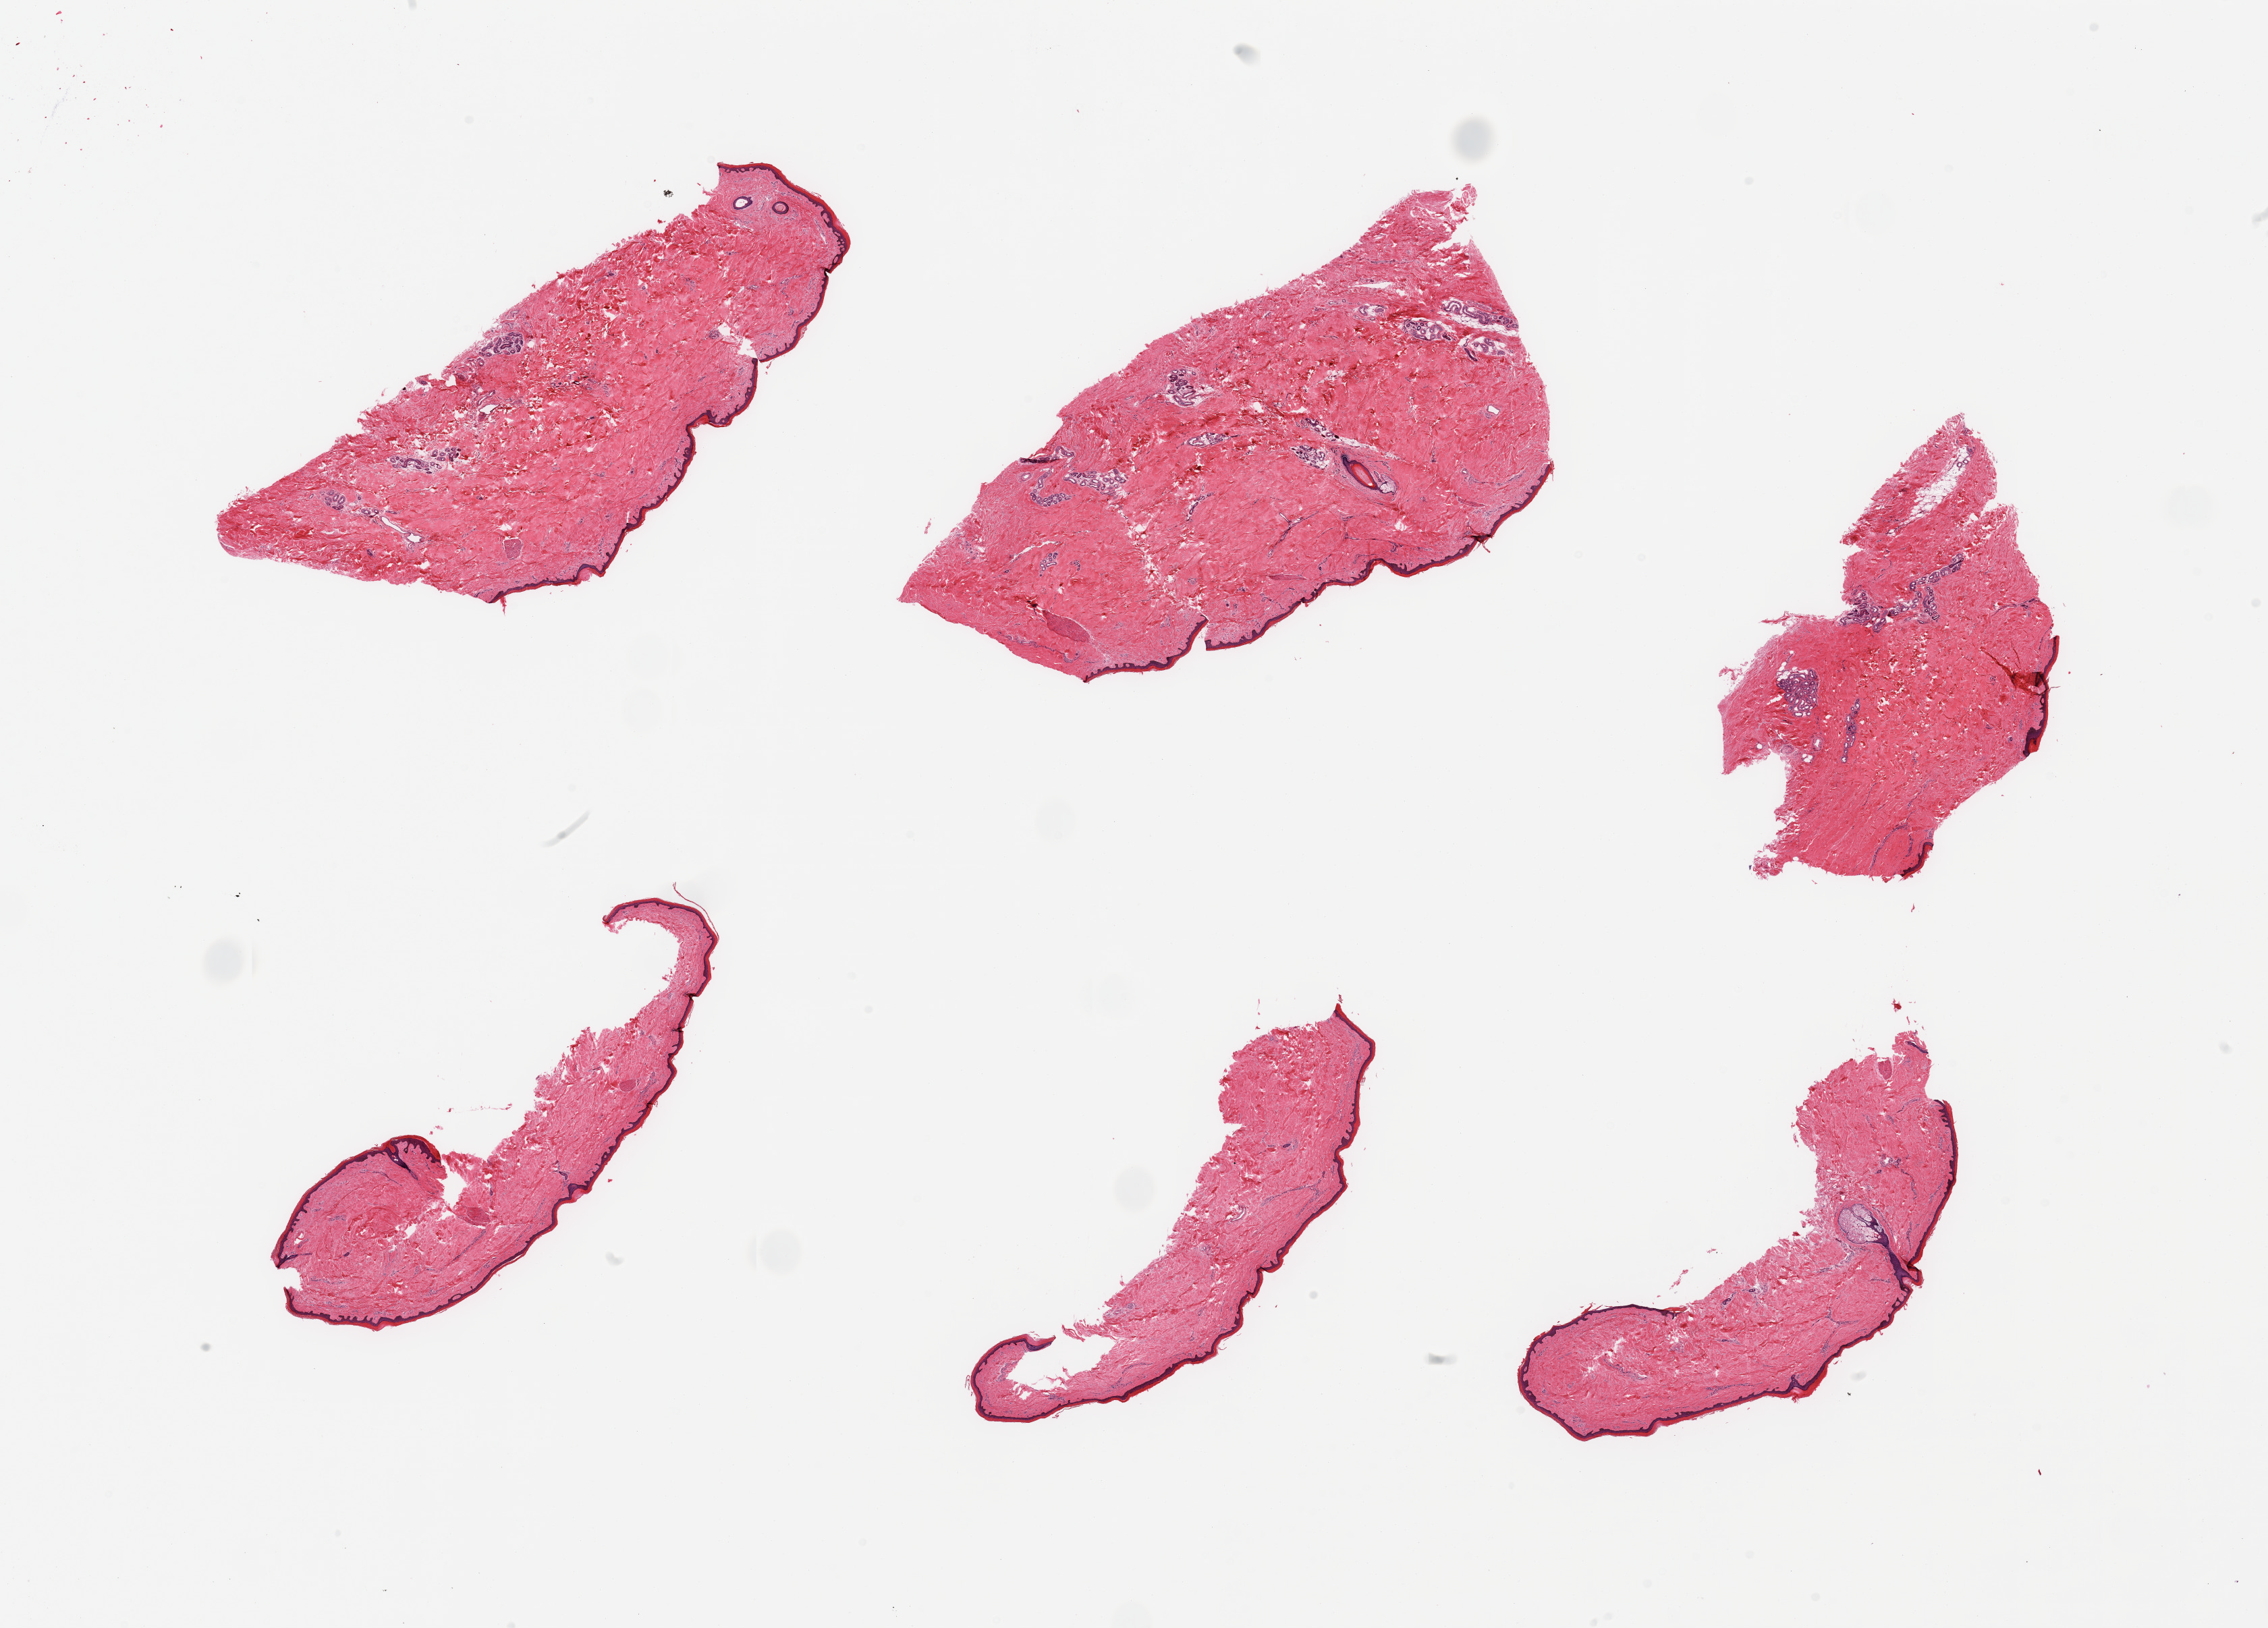
Haematoxylin and eosin whole-slide image, brightfield — a low-resolution overview of the entire scanned area, about 26.6 x 19.1 mm, PAXgene-fixed, paraffin-embedded tissue, section of skin of lower leg (target tissue), tissue donor sample. Donor: male.
Reviewer comment on this tissue sample: 6 pieces; well trimmed skin;minimal dermal fat.